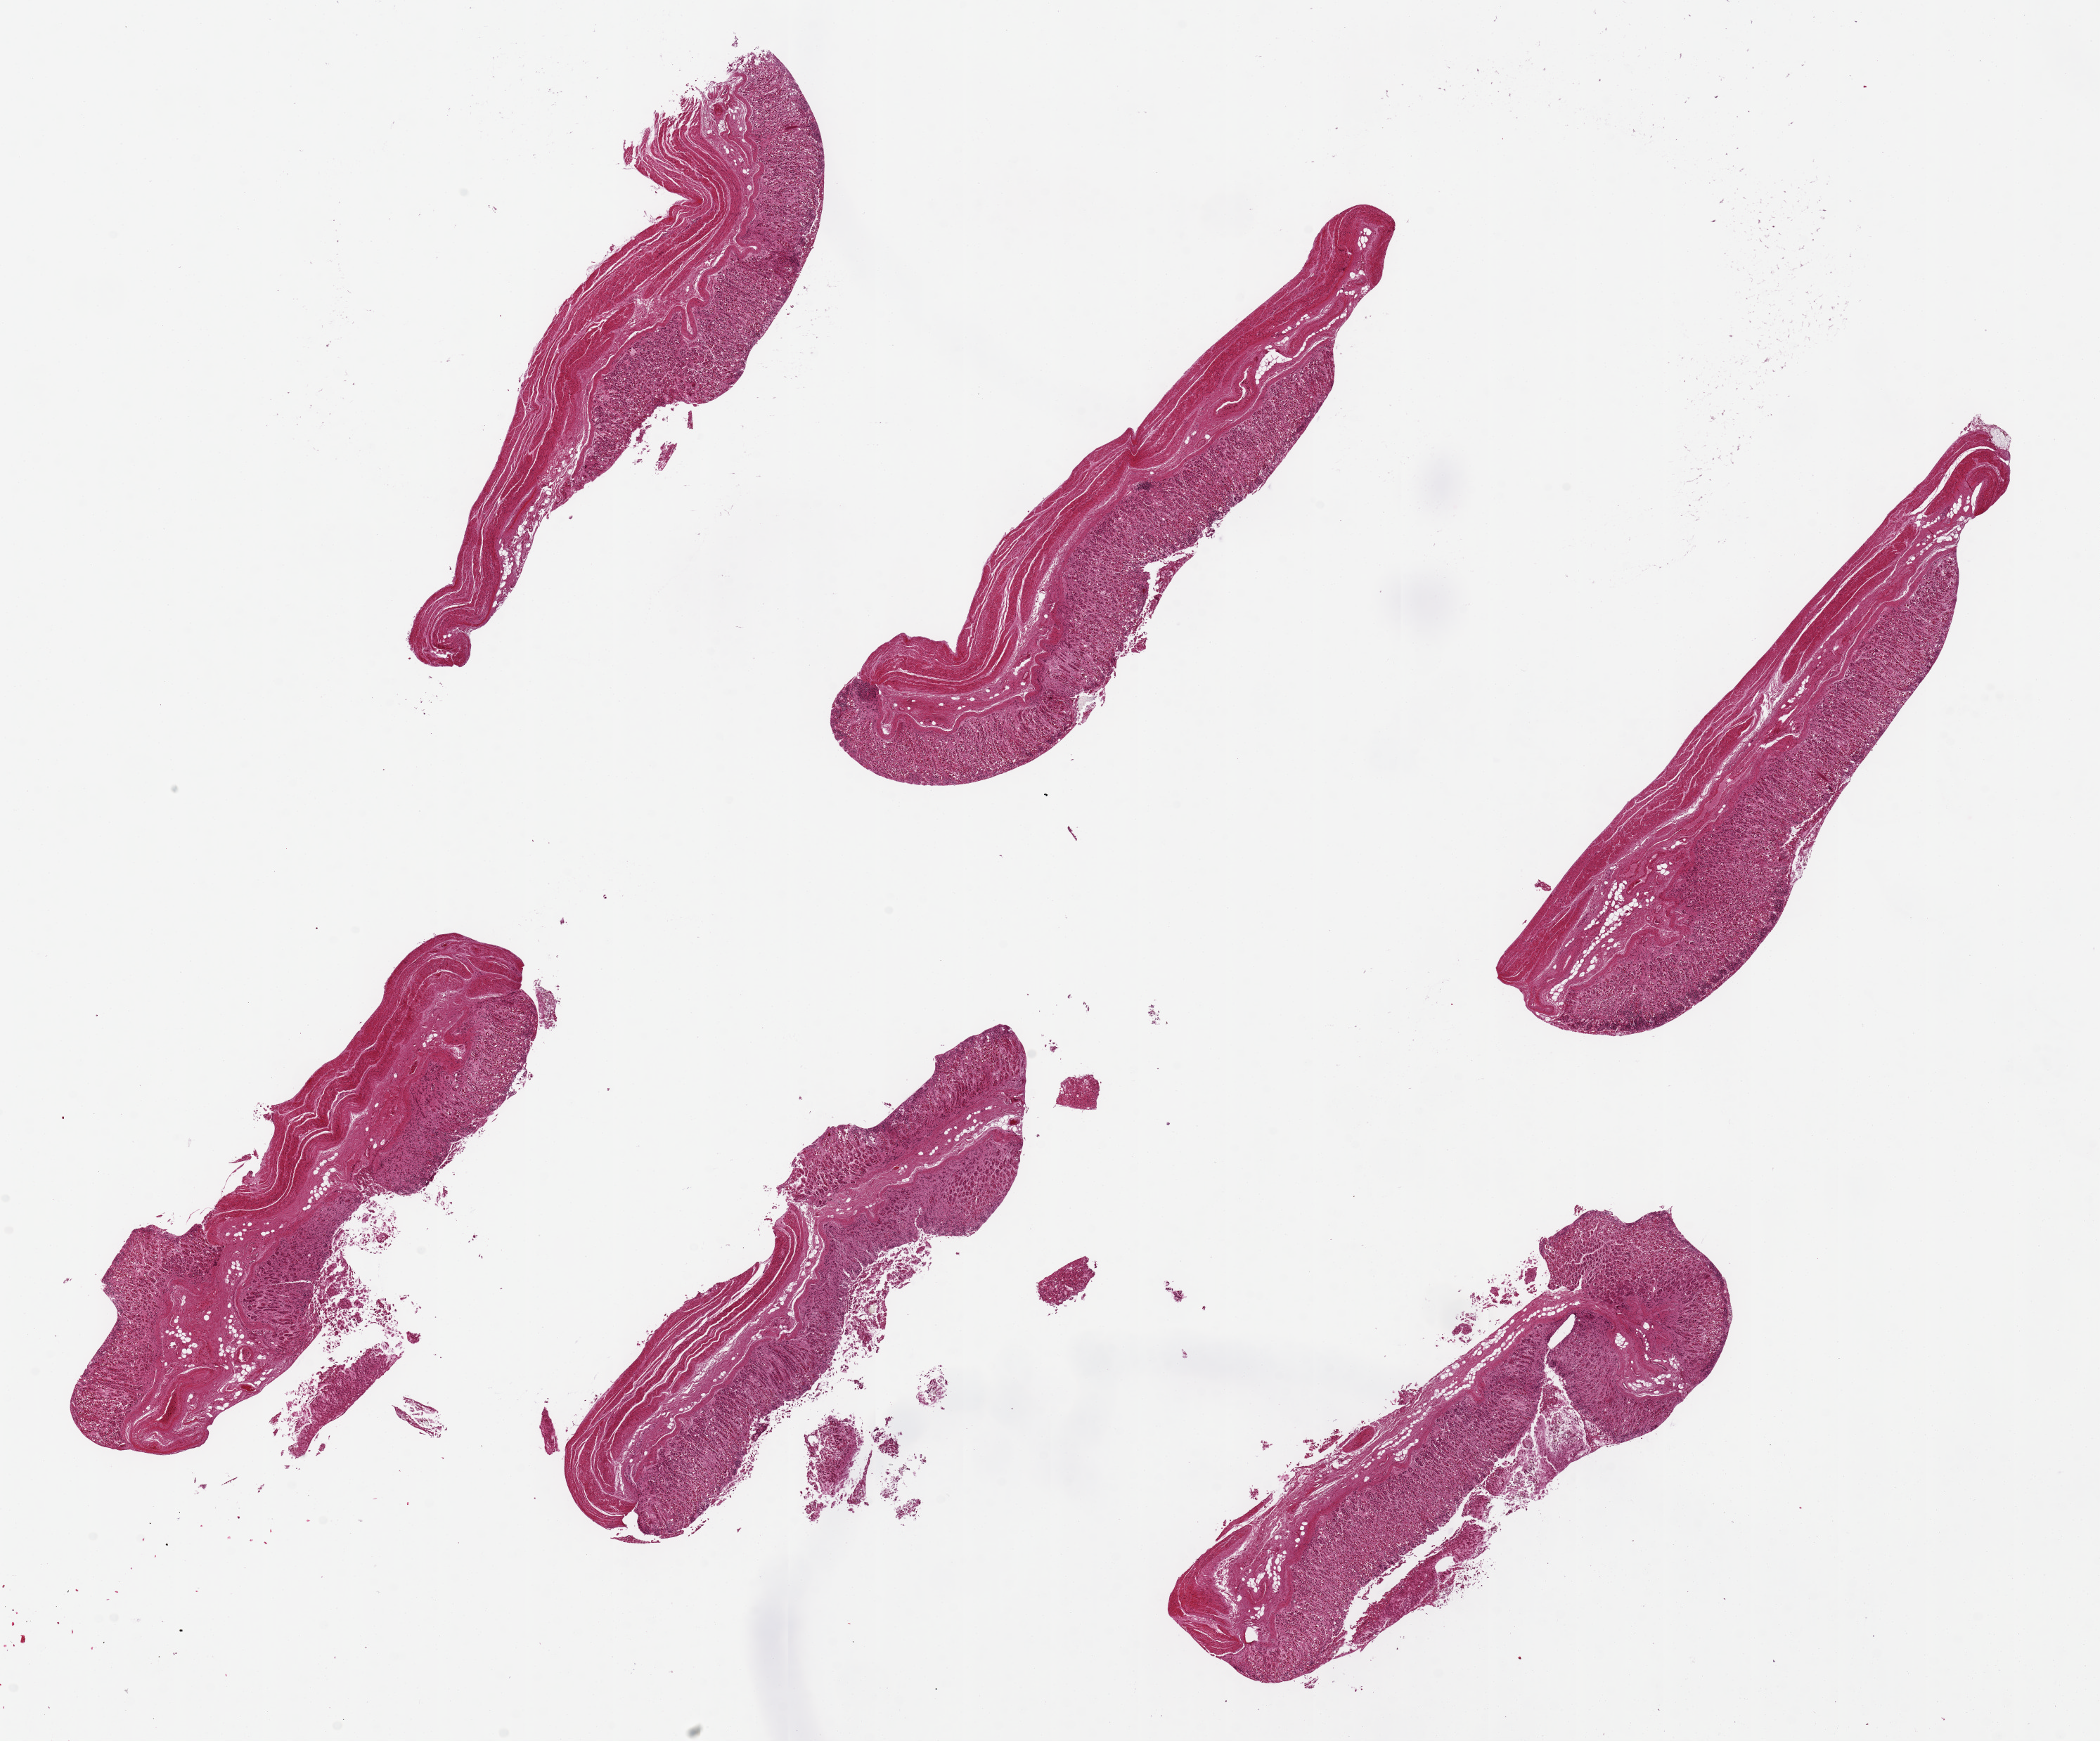
Whole-slide image, hematoxylin and eosin (H&E) stain — shown as a low-resolution overview of the whole scanned area (about 23.6 x 19.6 mm). PAXgene-fixed paraffin-embedded (PFPE) section. Section of stomach (target tissue). Donor tissue sample. Donor sex: male.
Review note (as recorded): 6 pieces, mucosa ~40% thickness but badly autolyzed ~8x2mm.